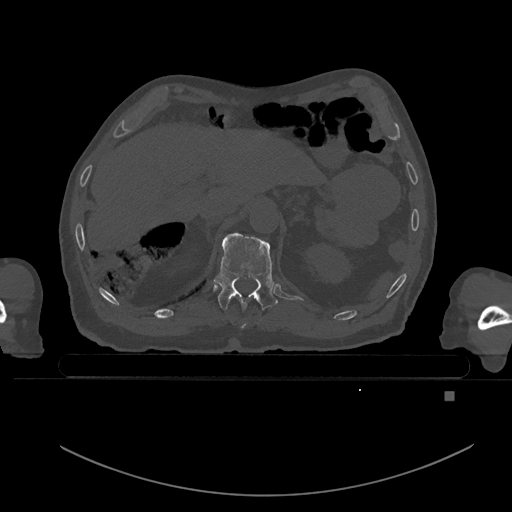
CT including the spine, one axial slice. Position 37 of 969 along the scan axis. Bone window (W 1800 / L 400 HU). 0.5 mm slice thickness. 512 × 512 image matrix. Patient: male, 82 years. Case-level facts recorded for this patient, not image findings: primary cancer: prostate.
Outlined on this slice (semi-automatically segmented with operator editing):
- T10 vertebra: bounding box <240,323,247,328> (left, top, right, bottom; pixels)
- T11 vertebra: <214,232,278,311>